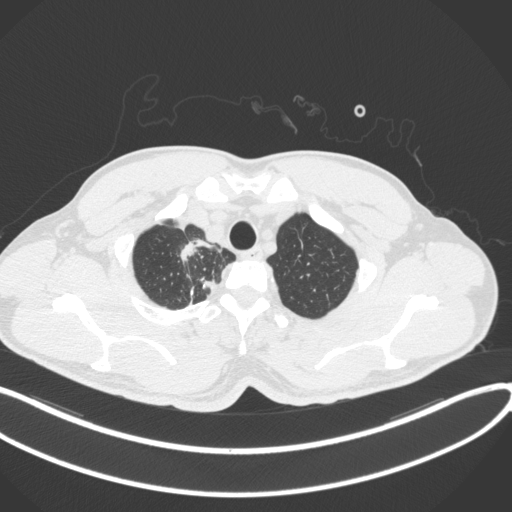
Chest CT, one axial slice; position 335 of 391 along the scan axis; reconstruction kernel B31f; 120 kVp; lung window (W 1500 / L -600 HU); 1 mm slice thickness; 512 × 512 image matrix, field of view 400 × 400 mm. Patient: male, 48 years. From the clinical record (not read from this slice): clinical TNM (as recorded): T1c N1 M1.
Structures marked on this image (rectangle marked by the reading radiologist):
- lung tumour (recorded histology: adenocarcinoma): box from (x=176, y=238) to (x=215, y=267) px